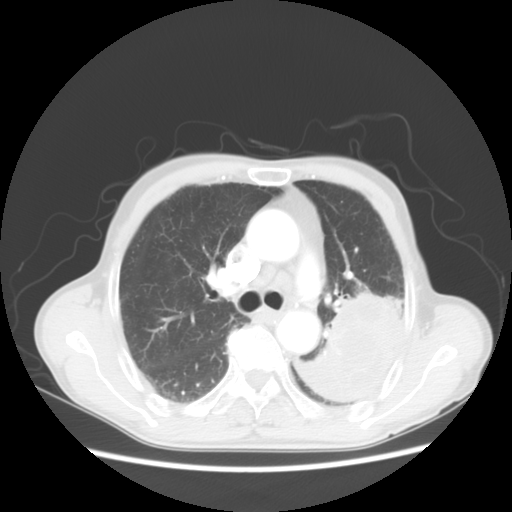
Chest CT, one axial slice. Position 34 of 51 along the scan axis. Reconstruction kernel STANDARD. 120 kVp. Lung window (W 1500 / L -600 HU). 5 mm slice thickness. 512 × 512 image matrix. Patient: male, 64 years. Case-level facts recorded for this patient, not image findings: clinical TNM (as recorded): T4 N0 M0; histopathological grade: G2-3.
Outlined on this slice (rectangle marked by the reading radiologist):
- lung tumour (recorded histology: squamous cell carcinoma): bounding box <312,295,397,413> (left, top, right, bottom; pixels)